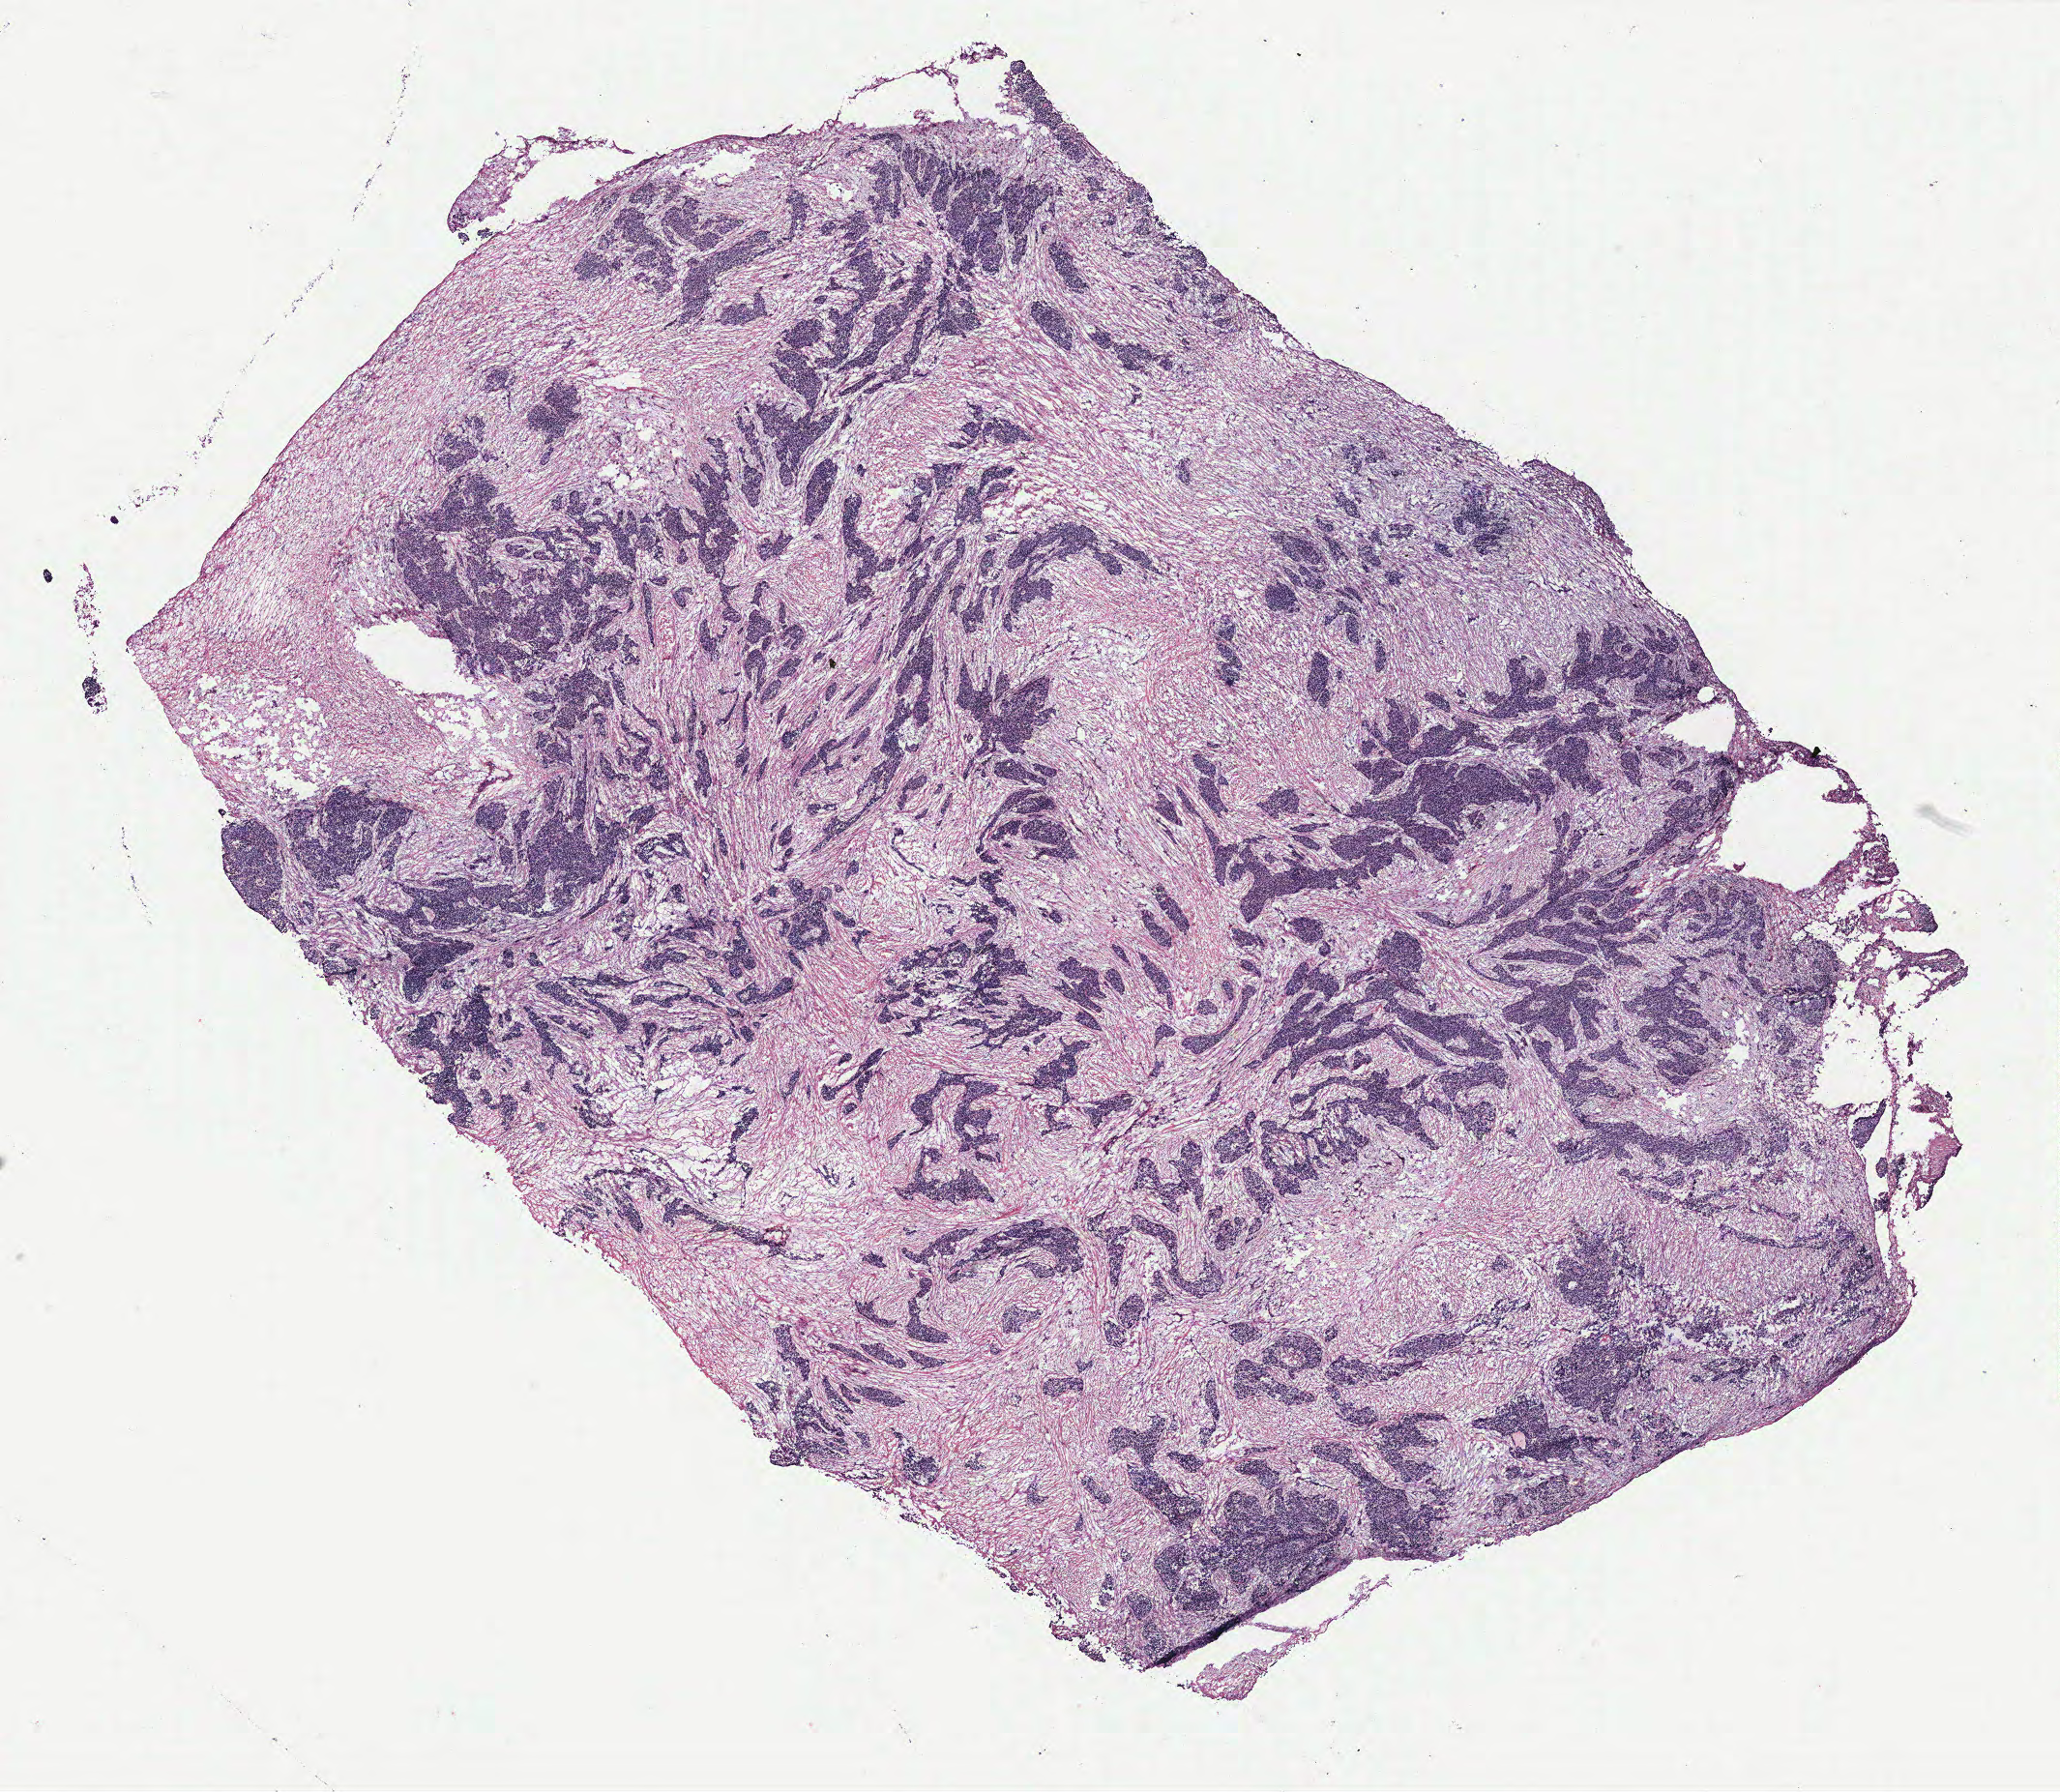
H&E whole-slide image — a low-resolution overview of the entire scanned area, about 17.0 x 14.8 mm; ovary, tumour tissue. Patient: female, age 70 years.
* primary tumour site (as recorded): peritoneum
* histologic diagnosis: Serous adenocarcinoma, NOS